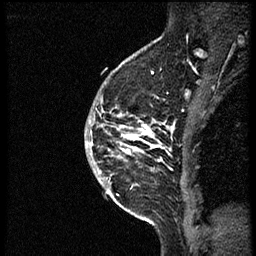
Breast MRI (dynamic contrast-enhanced), one sagittal slice. Slice 42 of 56 in the series (ordered by position). Dynamic contrast-enhanced study with each time point stored as its own series, time point 2 of 3 at this slice position (early post-contrast, ordered by acquisition time). 1.5 T. TE 4.2 ms, TR 21.3 ms. 2 mm slice thickness. 256 × 256 image matrix. Female patient, age 41 years. Case-level facts recorded for this patient, not image findings: setting: breast cancer imaged before/during neoadjuvant chemotherapy; receptor status: HER2-positive.
Structures marked on this image (semi-automatically segmented with operator editing):
- analysis volume of interest (the breast-tissue region the enhancement analysis was run in; not a lesion): bounding box <91,73,175,205> (left, top, right, bottom; pixels)
- tumour enhancement mask (voxels above the 100 % enhancement threshold inside the analysis volume of interest): <98,119,167,180>